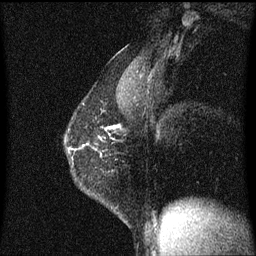
Breast MRI (dynamic contrast-enhanced), one sagittal slice. Position 41 of 60 along the scan axis. Dynamic contrast-enhanced series, image 2 of 3 at this slice position (ordered by acquisition). 1.5 T. TE 4.2 ms, TR 8.4 ms. 256 × 256 image matrix, field of view 200 × 200 mm. Patient: female, 40 years.
Annotated regions visible in this slice (semi-automatically segmented with operator editing):
- analysis volume of interest (the breast-tissue region the enhancement analysis was run in; not a lesion): bounding box [x1, y1, x2, y2] px = [66, 126, 115, 185]
- tumour enhancement mask (voxels above the 70 % enhancement threshold inside the analysis volume of interest): [105, 126, 115, 131]